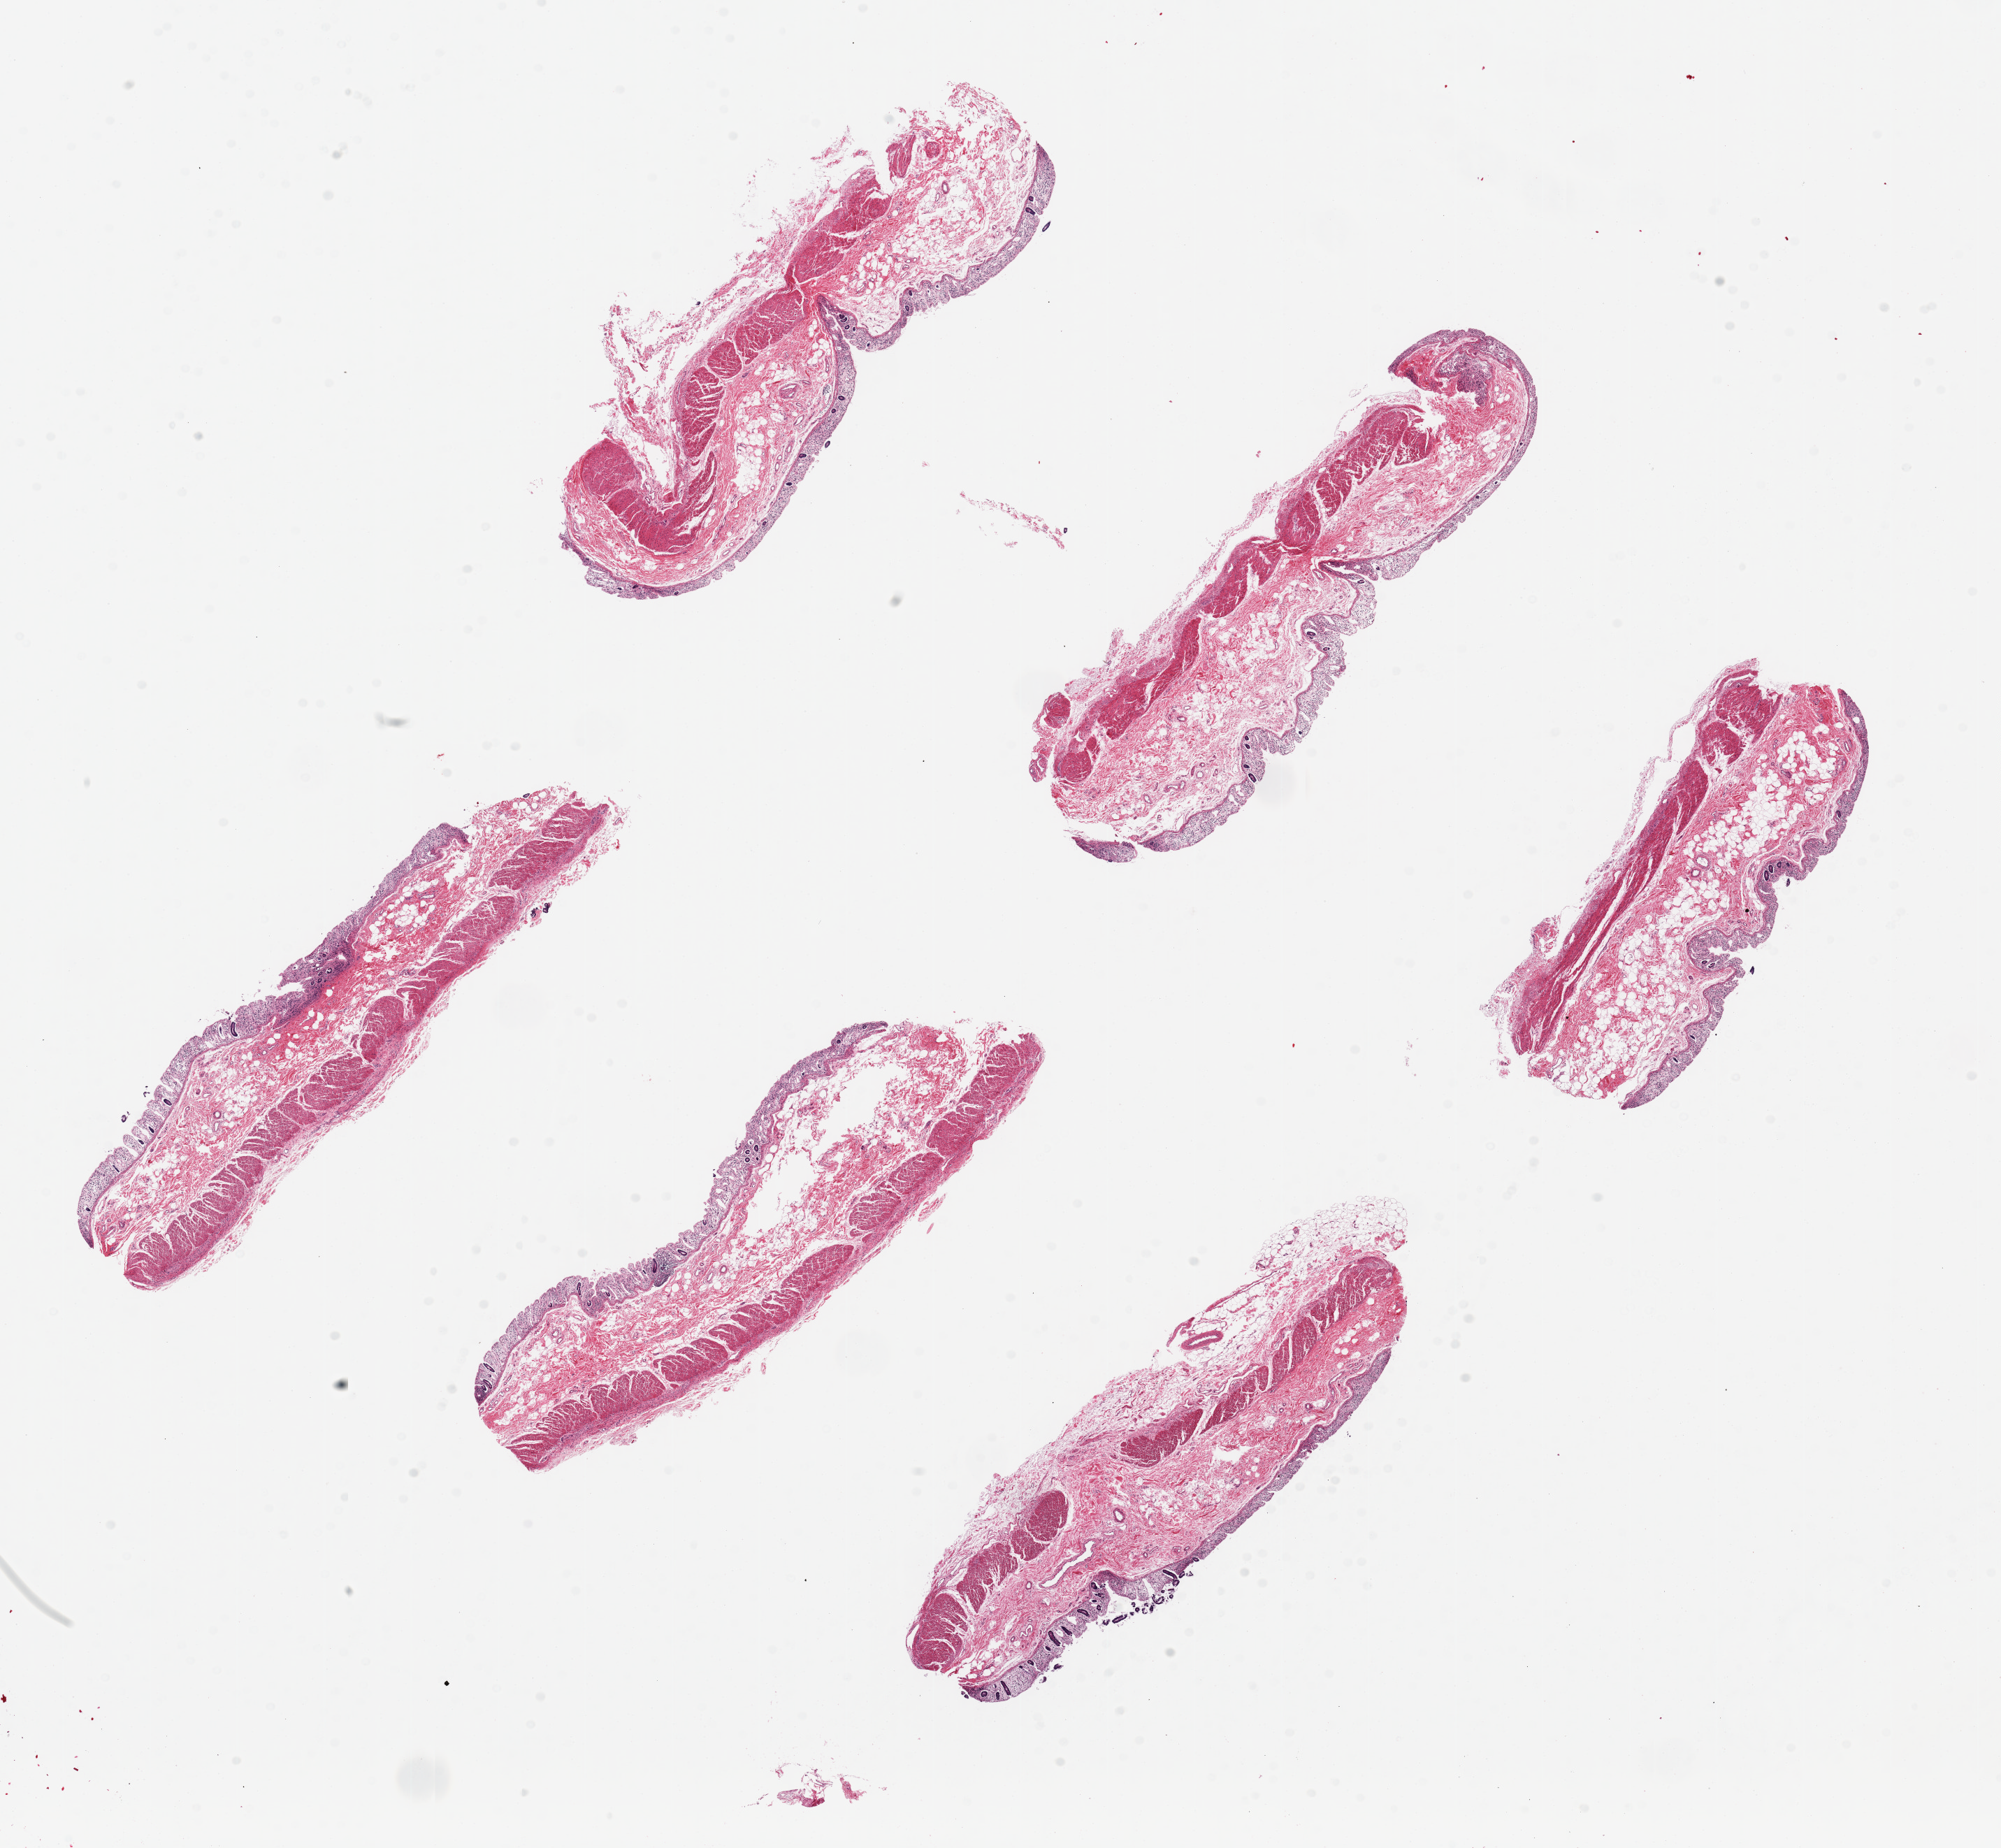
Hematoxylin and eosin (H&E) whole-slide image, whole scanned area (about 22.6 x 20.9 mm, acquisition: 20x scan) shown as a low-resolution overview, PAXgene-fixed paraffin-embedded (PFPE) section, section of transverse colon (target tissue), tissue donor sample. Donor sex: male.
* pathologist's review note for this sample: 6 pieces ~7x1.5mm. Mucosa badly autolyzed, ~10% thickness